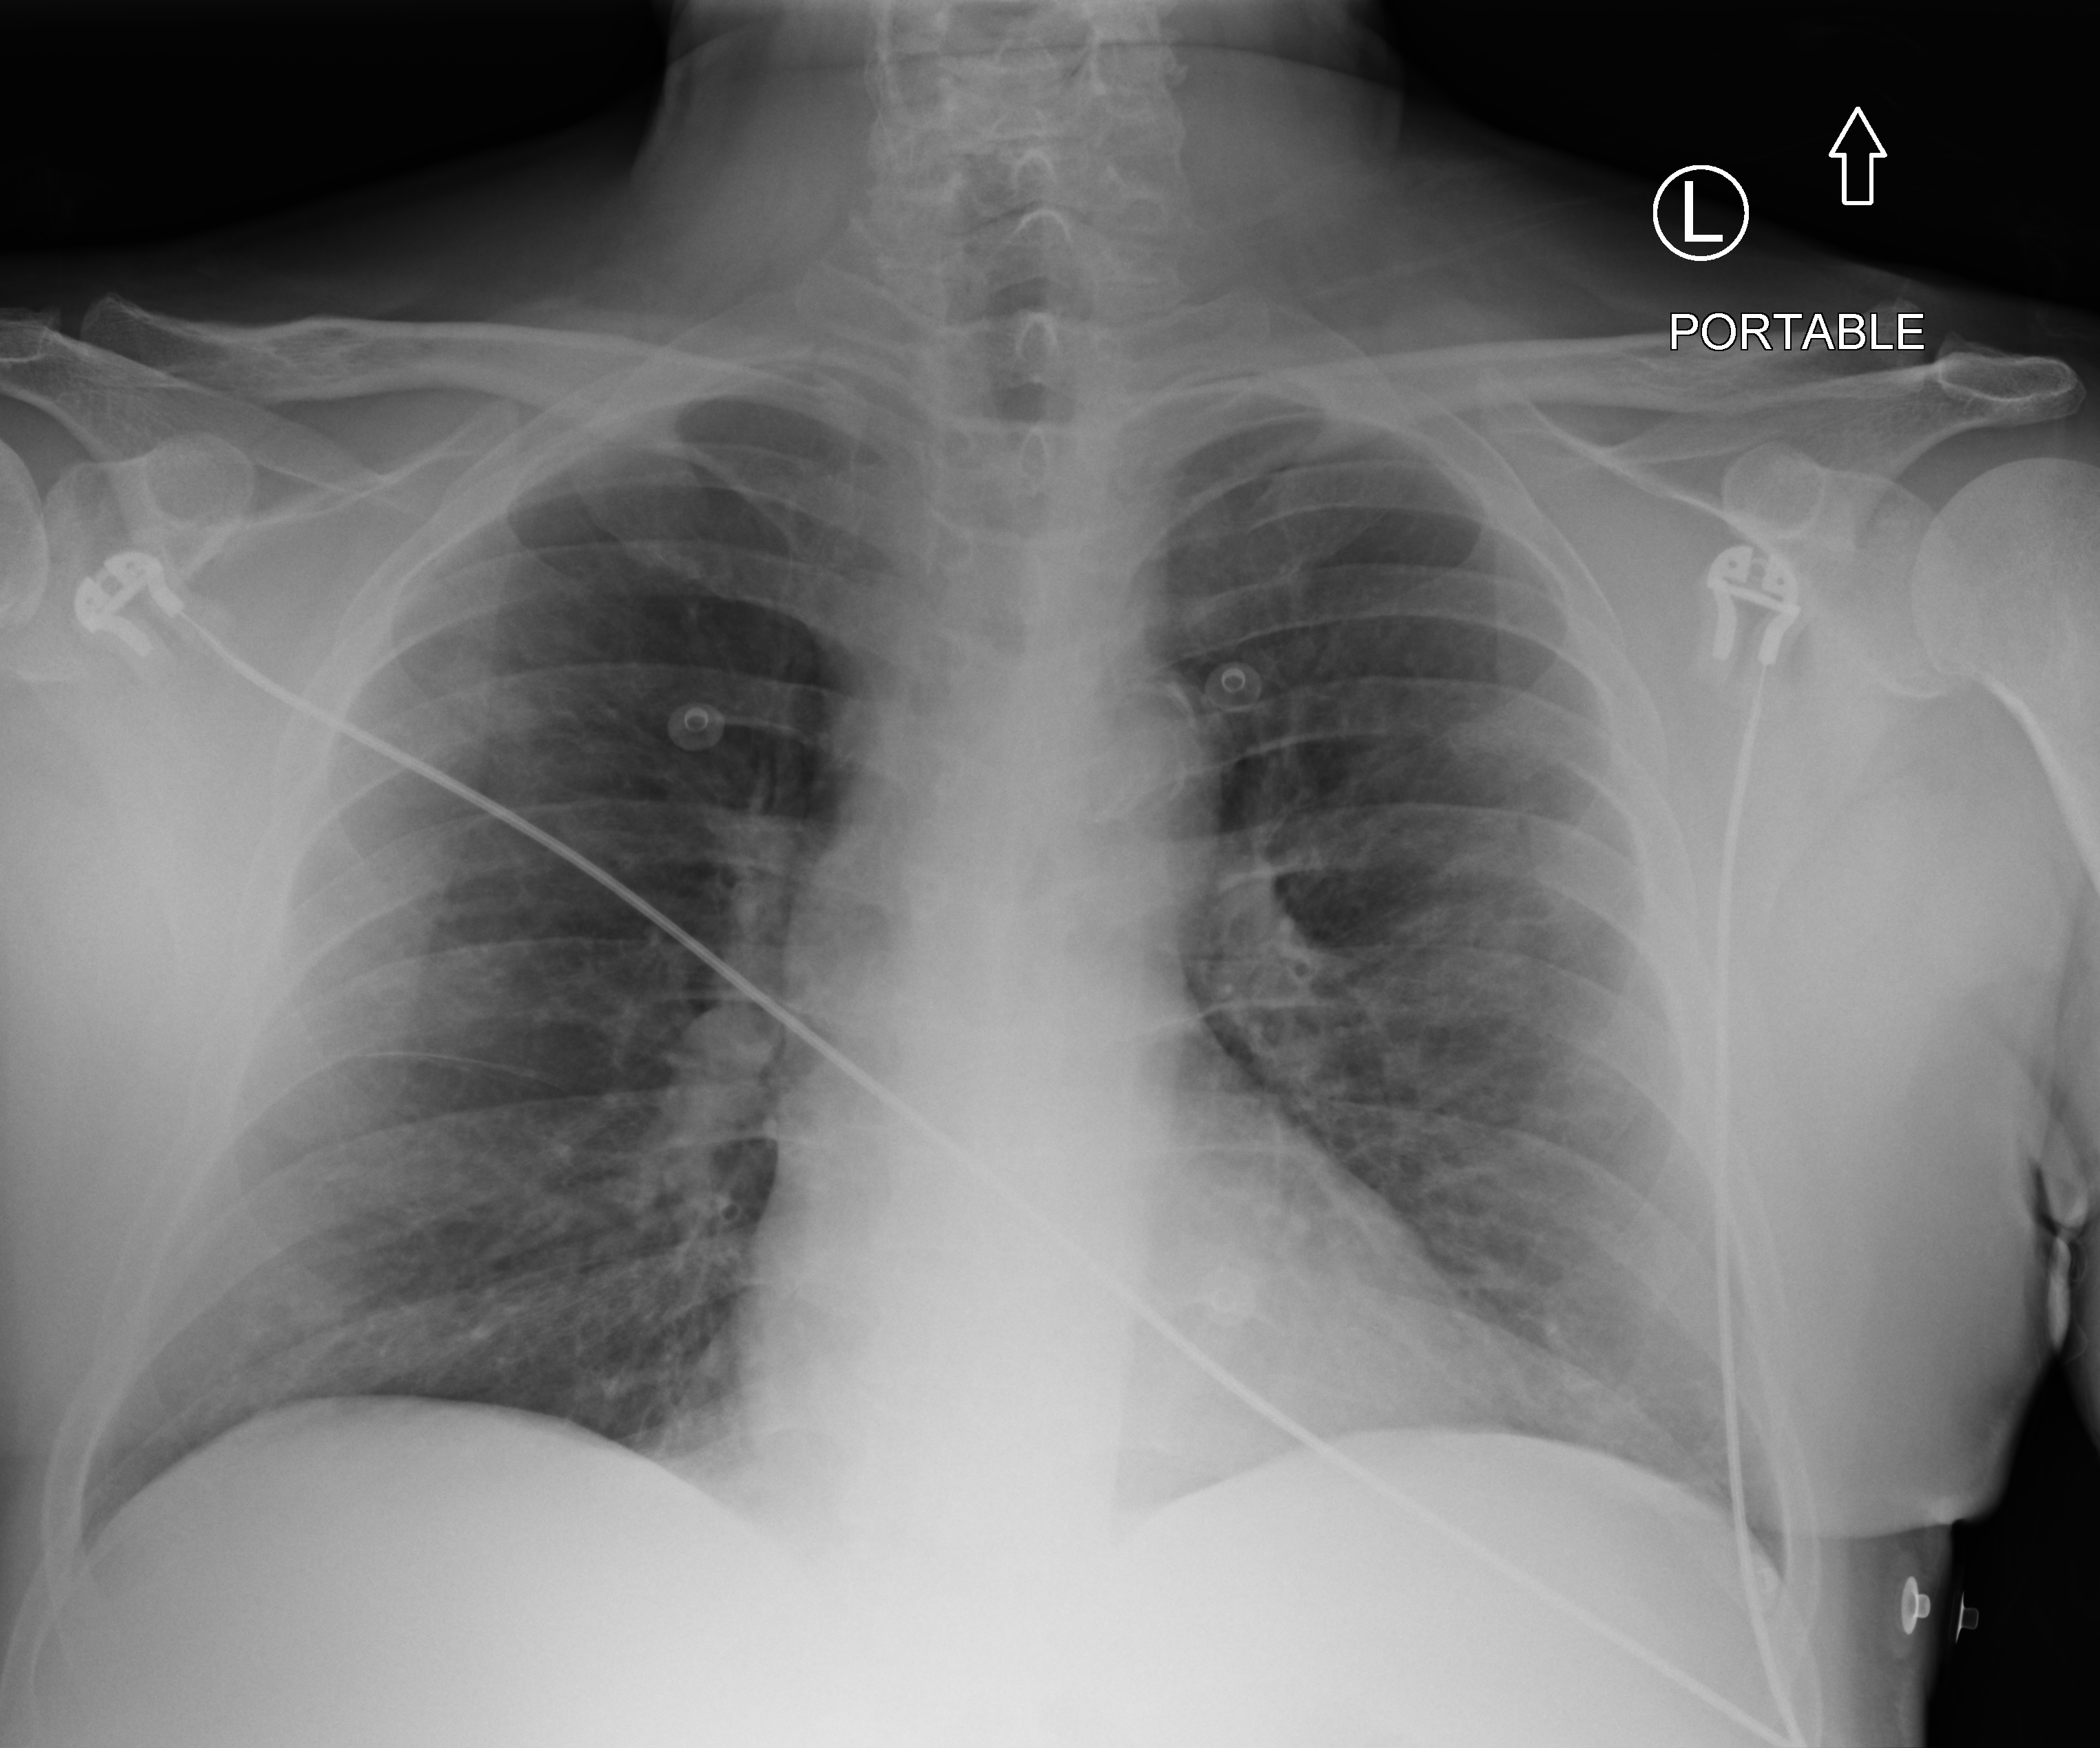
Chest X-ray (portable); anteroposterior (AP) projection. Male patient hospitalised with COVID-19, age 60–74 years.
Hospital-stay facts (about this admission, not read from this image; timing relative to this image not recorded):
- mechanically ventilated during this hospital stay: no